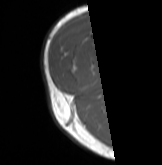
MRI of an extremity soft-tissue mass, one axial slice; position 11 of 61 along the scan axis; MR volume resampled by the dataset authors to the PET/CT grid (not the native acquisition matrix); 3.27 mm slice thickness; 162 × 165 image matrix, field of view 158 × 161 mm. Male patient. From the clinical record (not read from this slice): histological type: poorly differentiated synovial sarcoma; grade: high; site of the primary tumour: right buttock.
Outlined on this slice (expert contour drawn on MRI and transferred to this co-registered scan by the dataset authors):
- gross tumour volume including surrounding oedema: box from (x=68, y=50) to (x=92, y=78) px